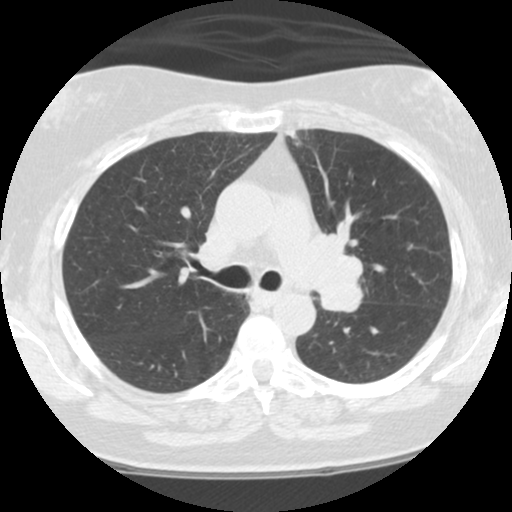
Axial slice from a low-dose chest CT screening exam, third annual screen, lung window (W 1500 / L -600 HU), 2.5 mm slice thickness, standard (soft-tissue) reconstruction kernel (STANDARD). Female, age 59 years at enrolment. Current smoker at enrolment.
• Expert-annotated lung lesion, bounding box (x1, y1, x2, y2) in pixels: (285, 213, 381, 325).
• Screening reader's record for this exam: no non-calcified nodule ≥4 mm recorded.
• Official screen result: positive, other.